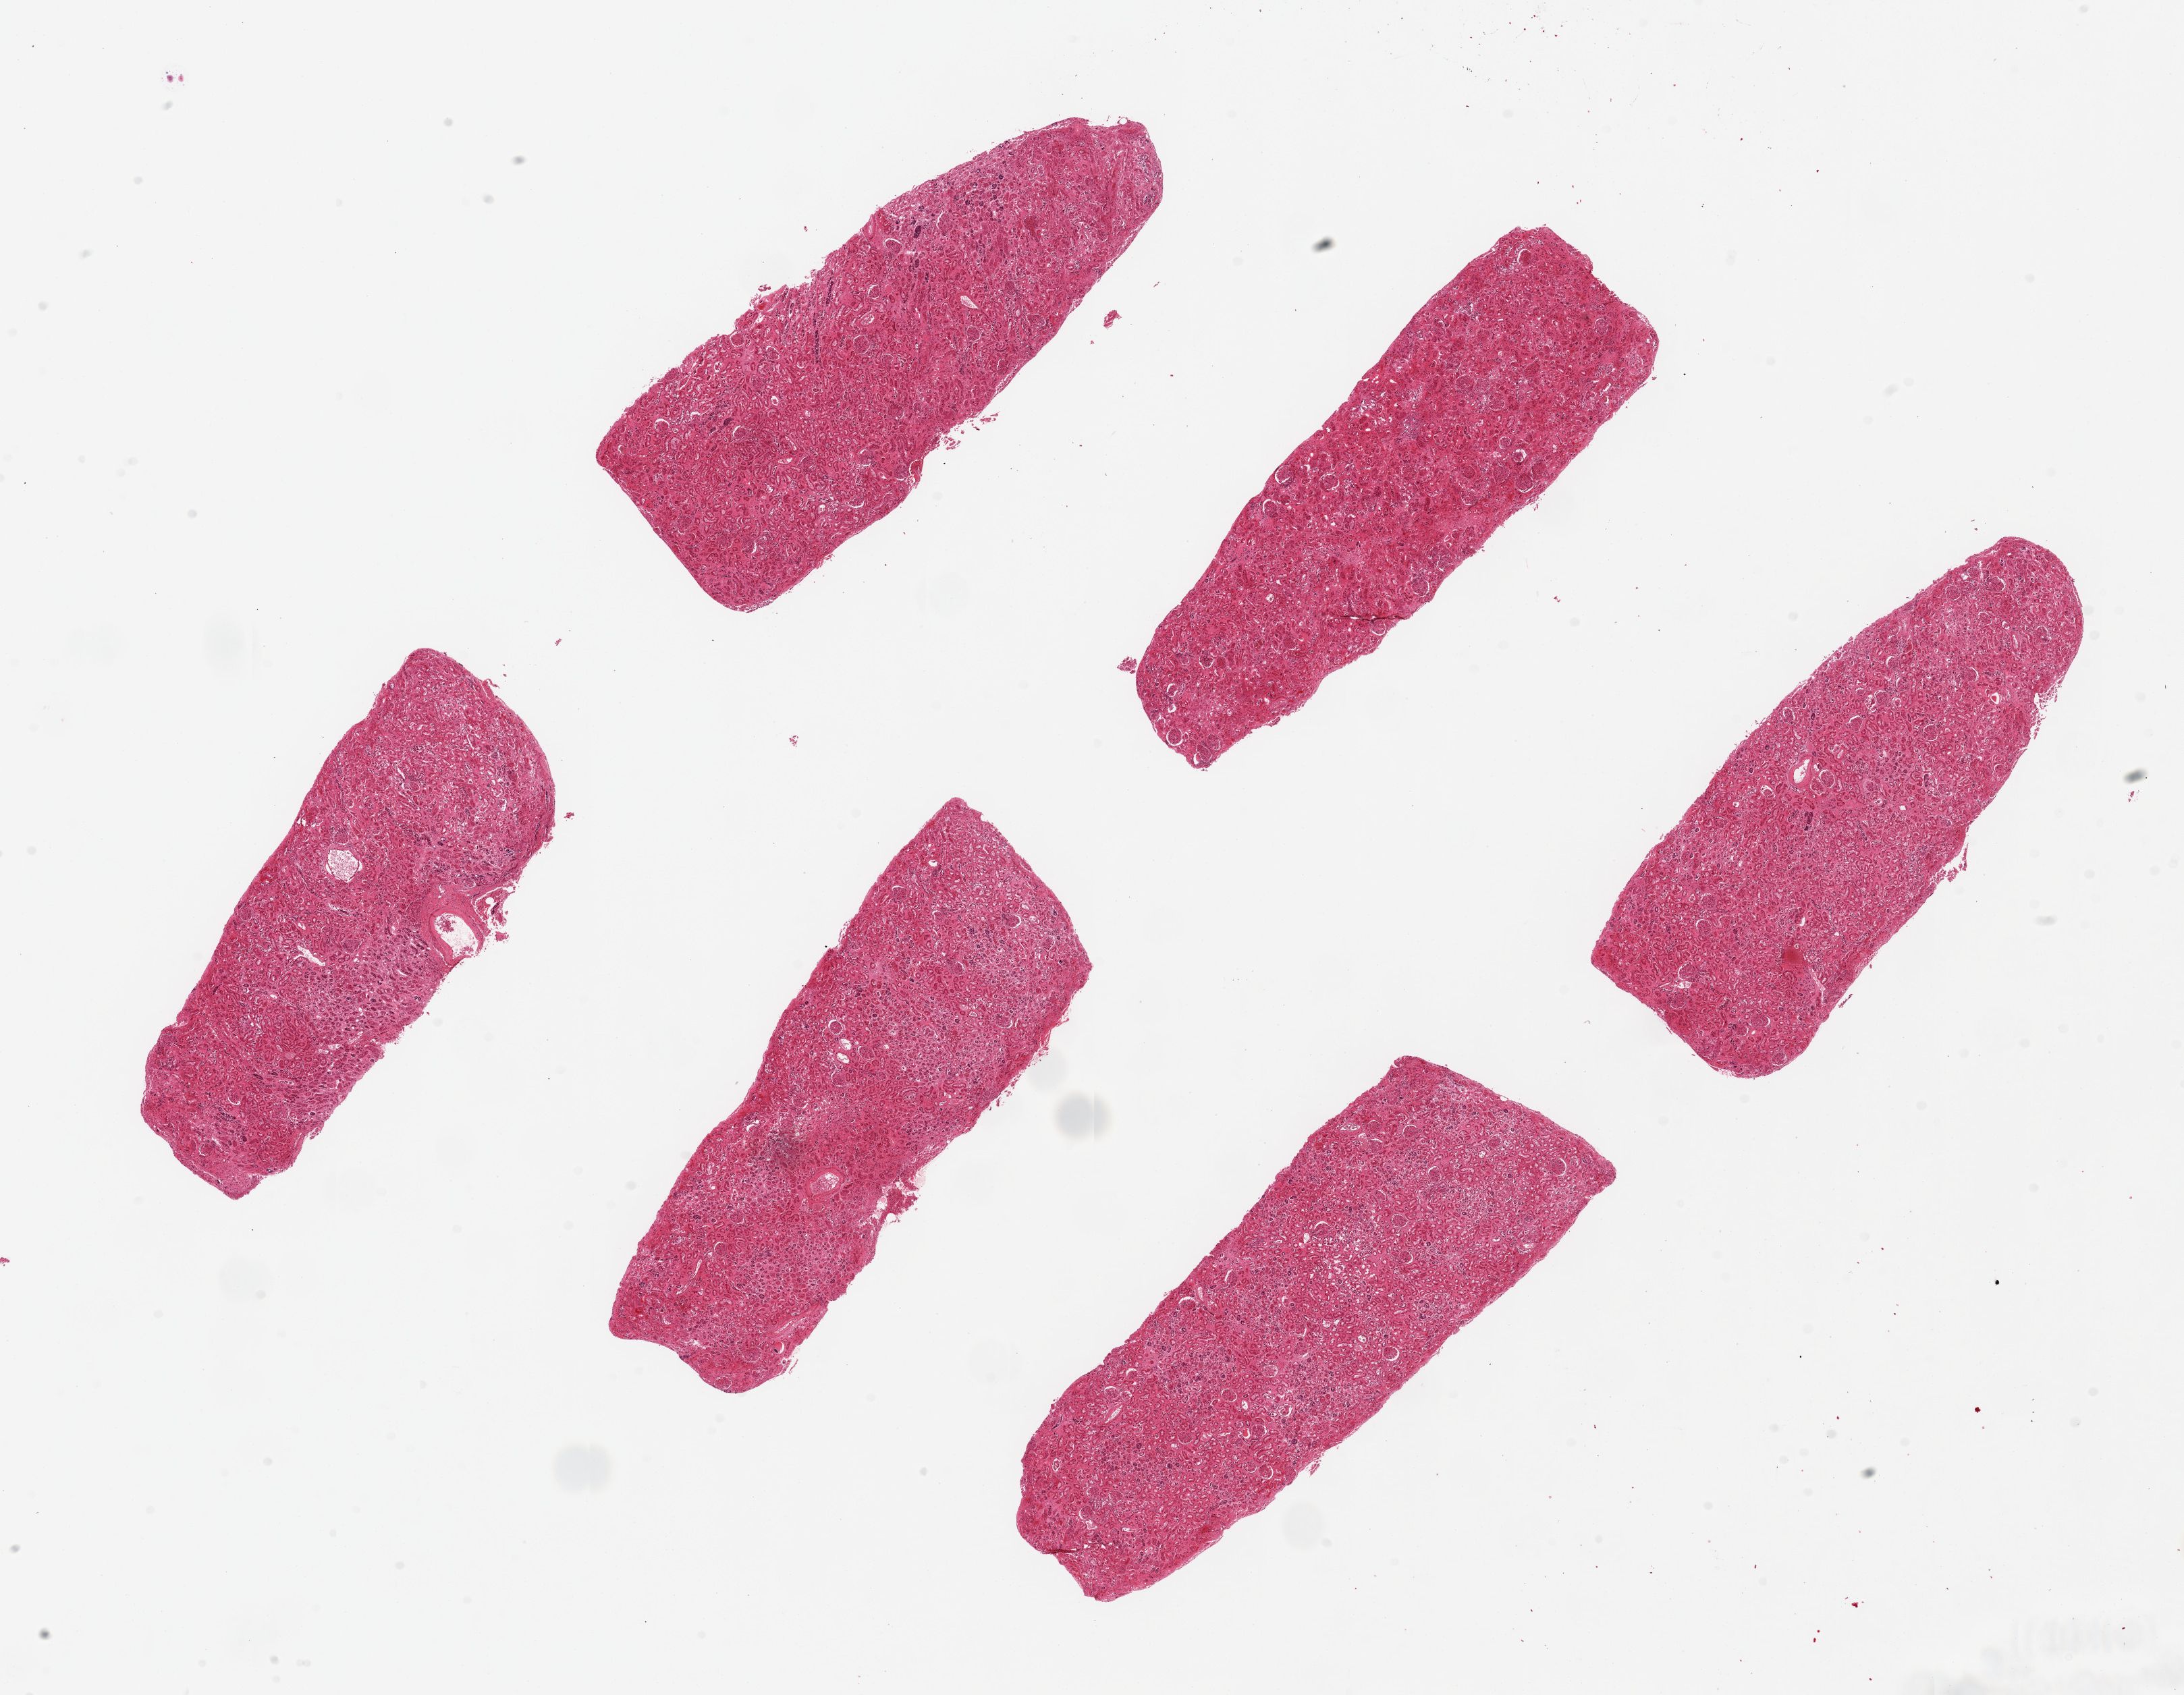
Haematoxylin and eosin whole-slide image — whole scanned area (about 25.6 x 19.9 mm, acquisition: 20x scan) shown as a low-resolution overview, PAXgene-fixed paraffin-embedded (PFPE) section, sampled site (target tissue): renal cortex, tissue donor sample. Male donor.
* pathologist's review note for this sample: 6 pieces ~7x3mm. Badly autolyzed